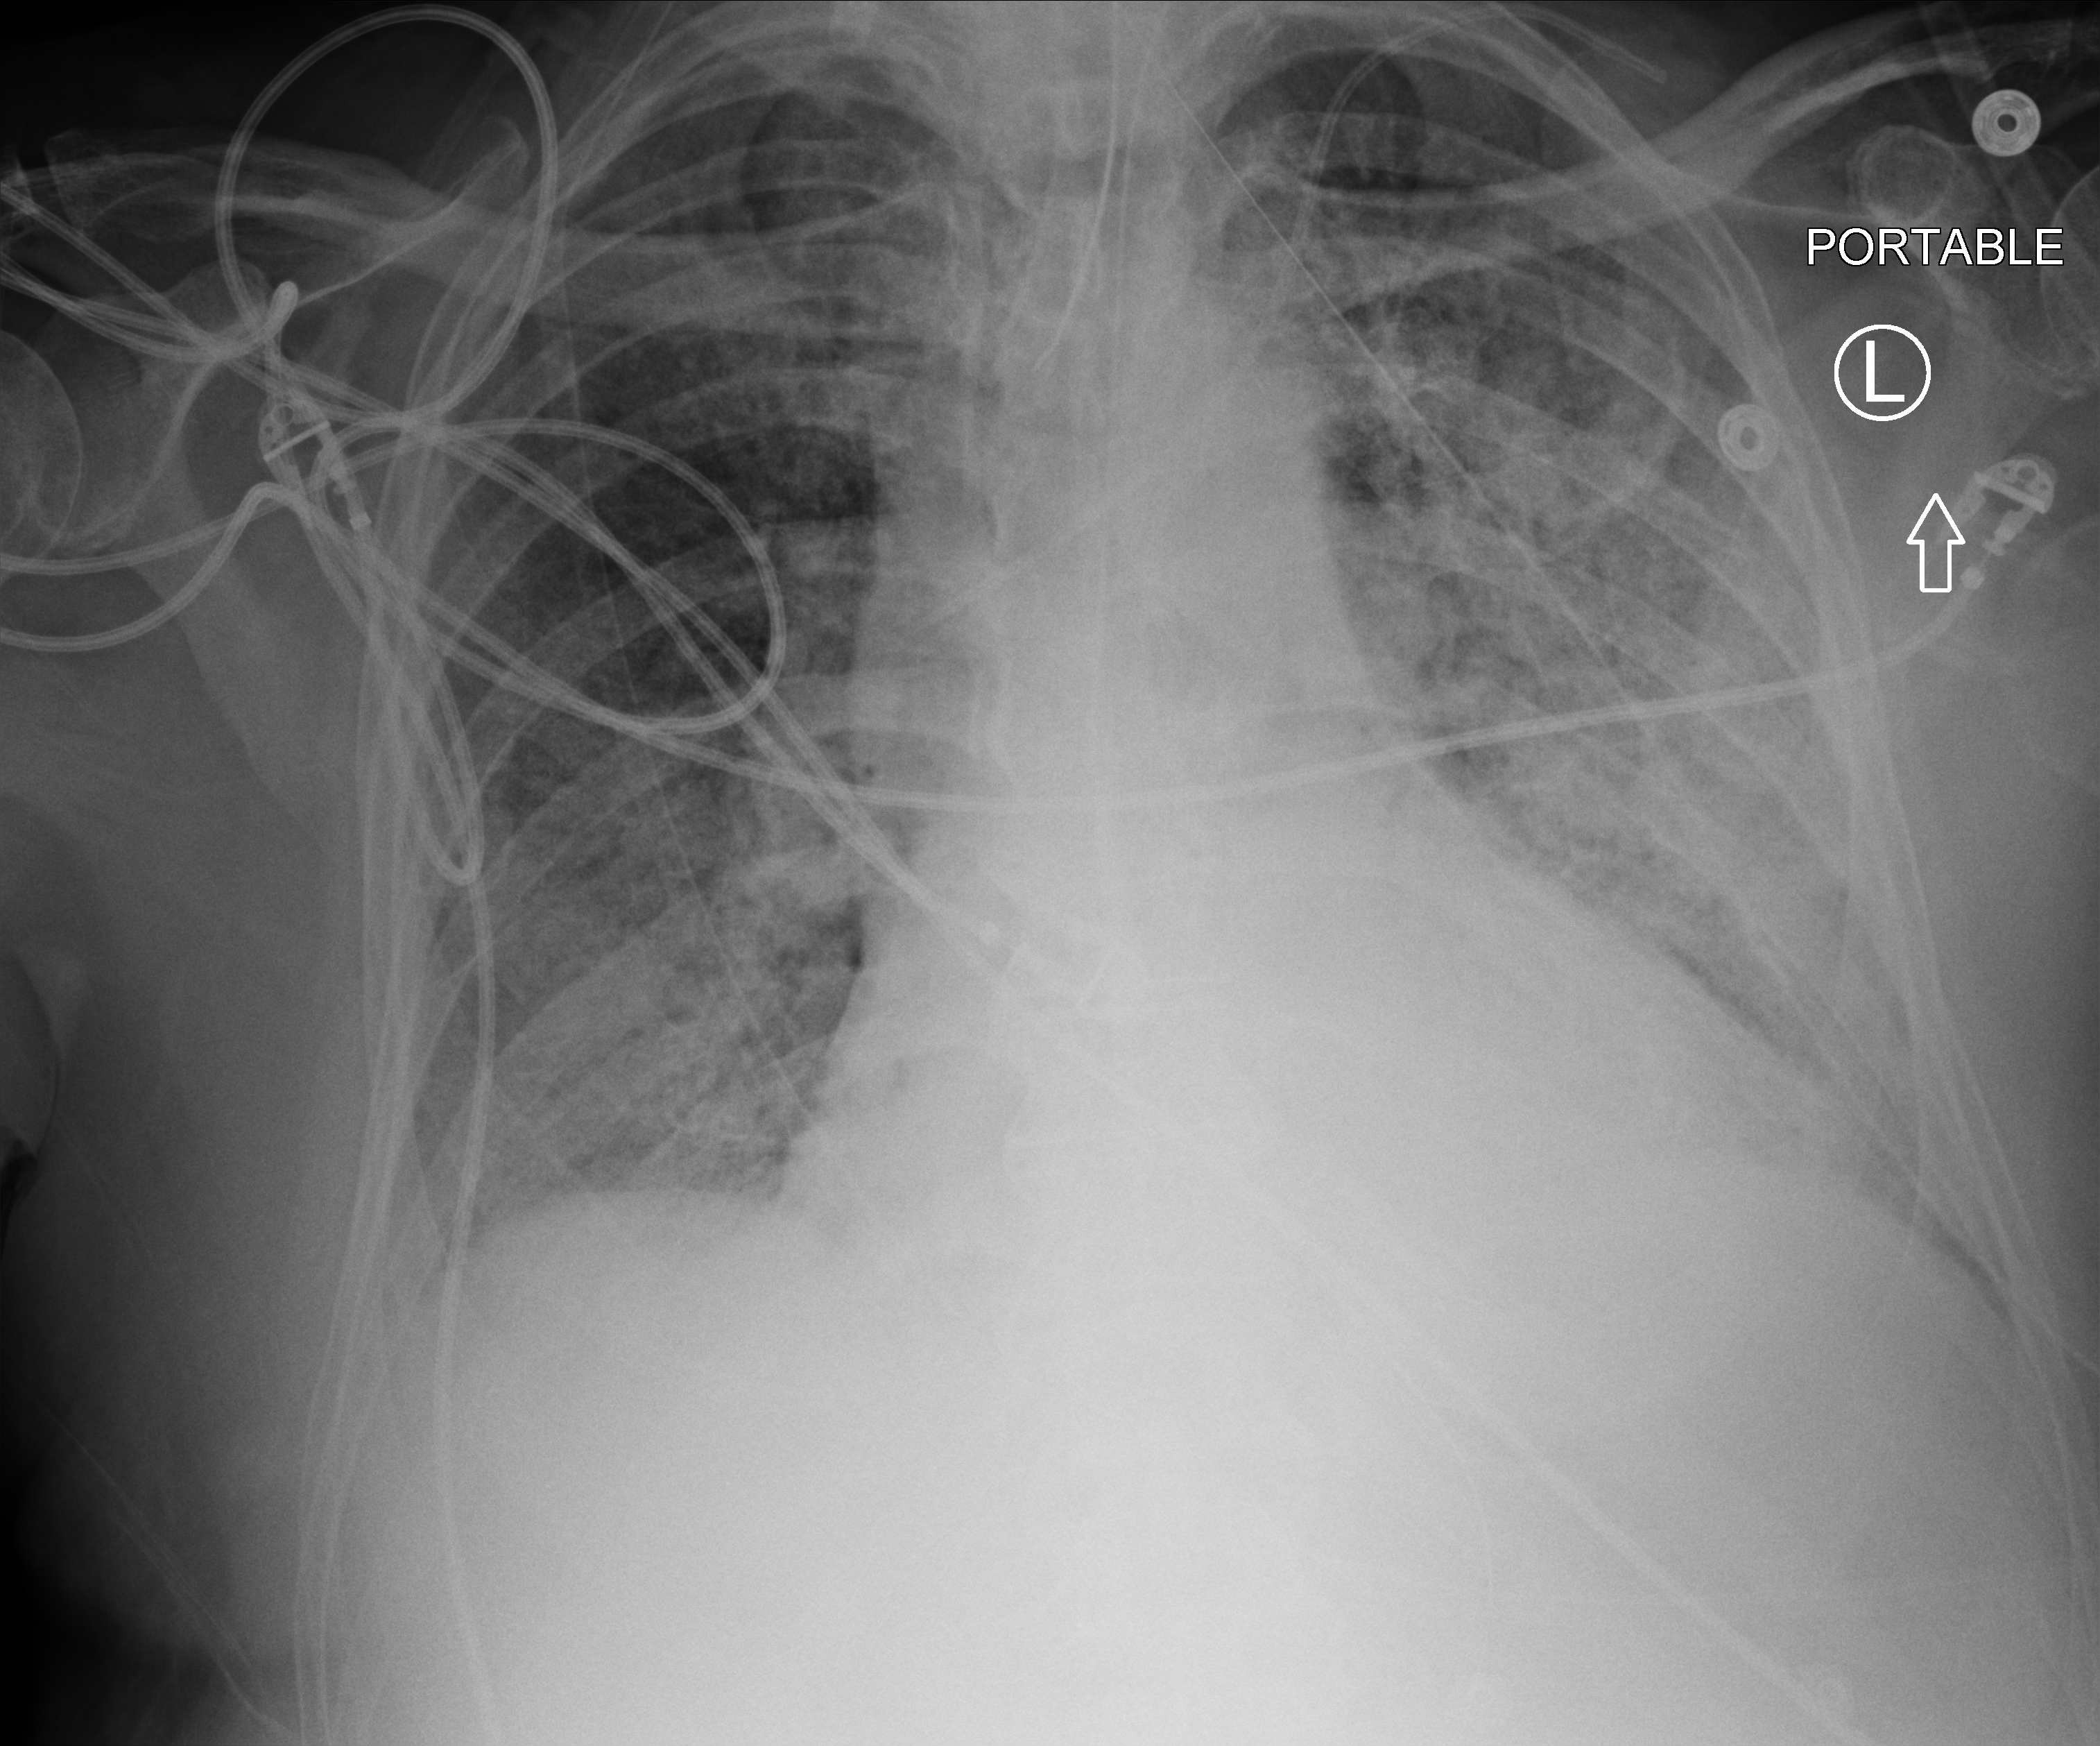
Bedside chest radiograph (computed radiography), anteroposterior (AP) projection. Patient hospitalised with COVID-19; male, aged 75–90 years.
Admission-level facts for this patient (not findings on this image; timing relative to this image not recorded):
- mechanically ventilated during this hospital stay: yes
- admitted to intensive care during this hospital stay: yes